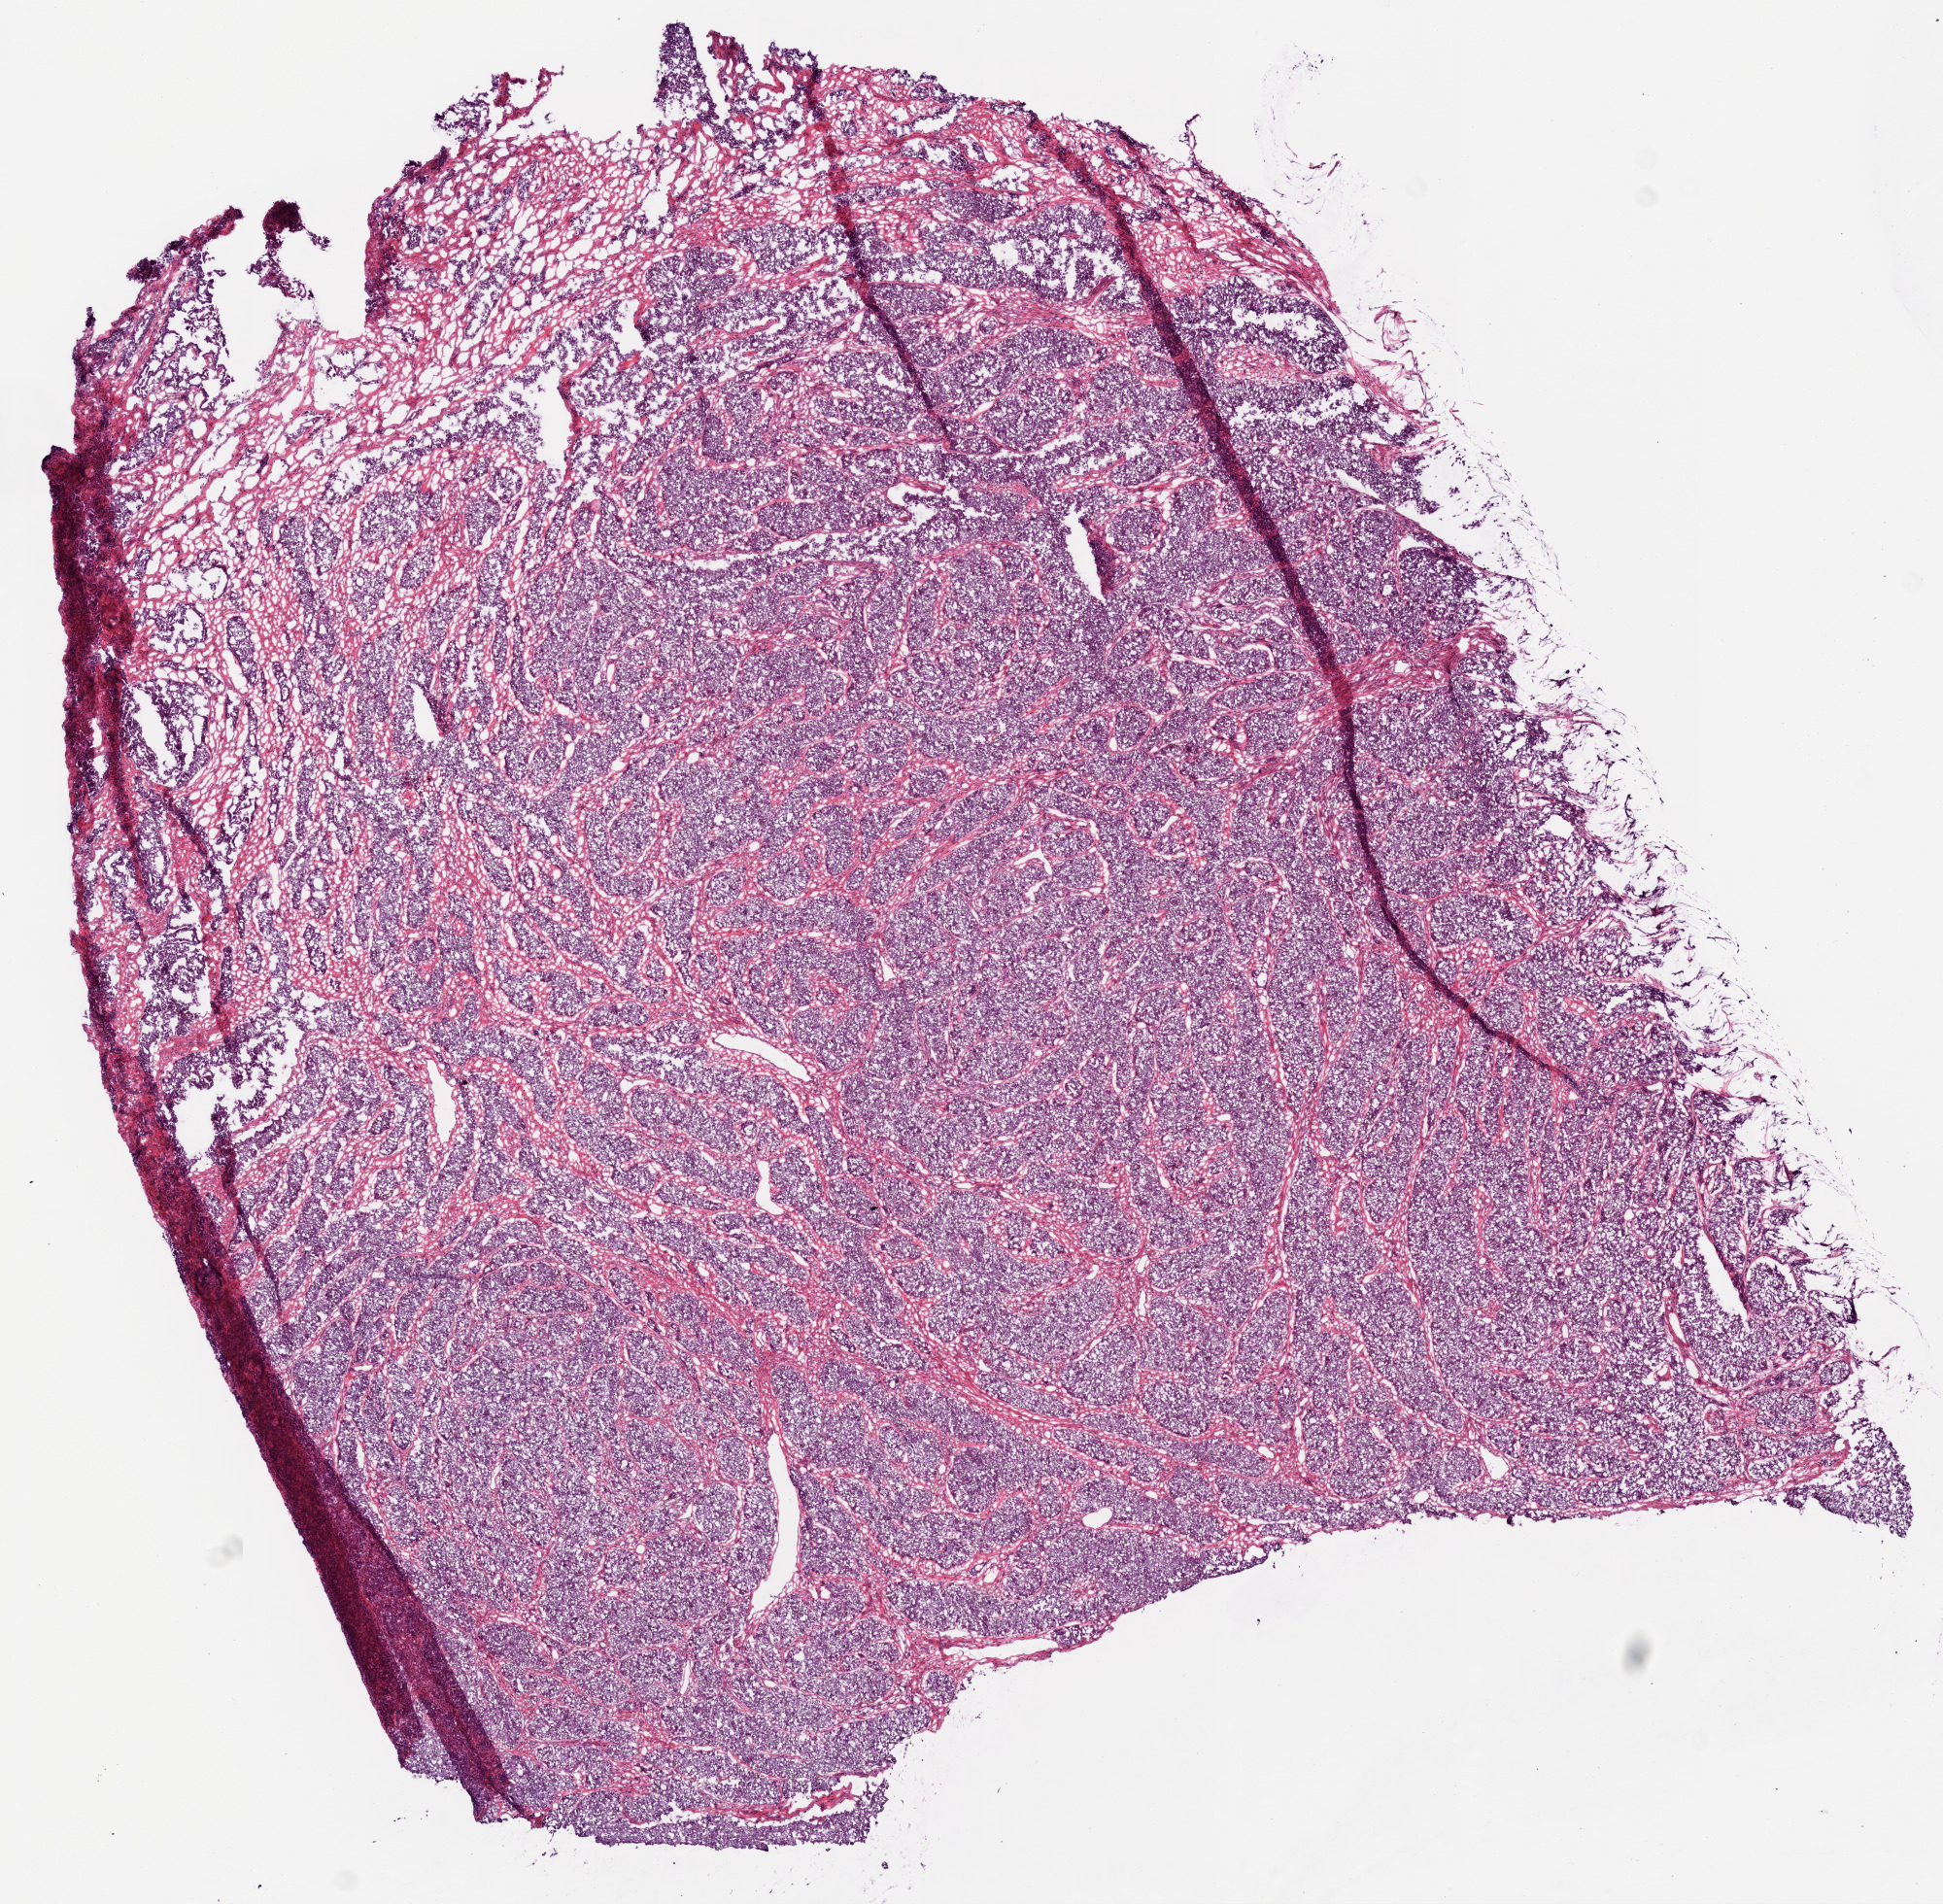
Whole-slide histology image, Hematoxylin and eosin (H&E) stained, whole scanned area (about 8.0 x 7.9 mm, acquisition: 20x scan) shown as a low-resolution overview, frozen section, primary tumour sample from the ovary. Female patient; age at initial diagnosis 74 years. Histologic grade: G3 (poorly differentiated). Composition of this section per pathologist review: tumour cells 95%, tumour nuclei 95%, normal cells 0%, stromal cells 5%, necrosis 0%.
Diagnosis: Serous cystadenocarcinoma, NOS. Laterality: bilateral. FIGO stage: IIIC.